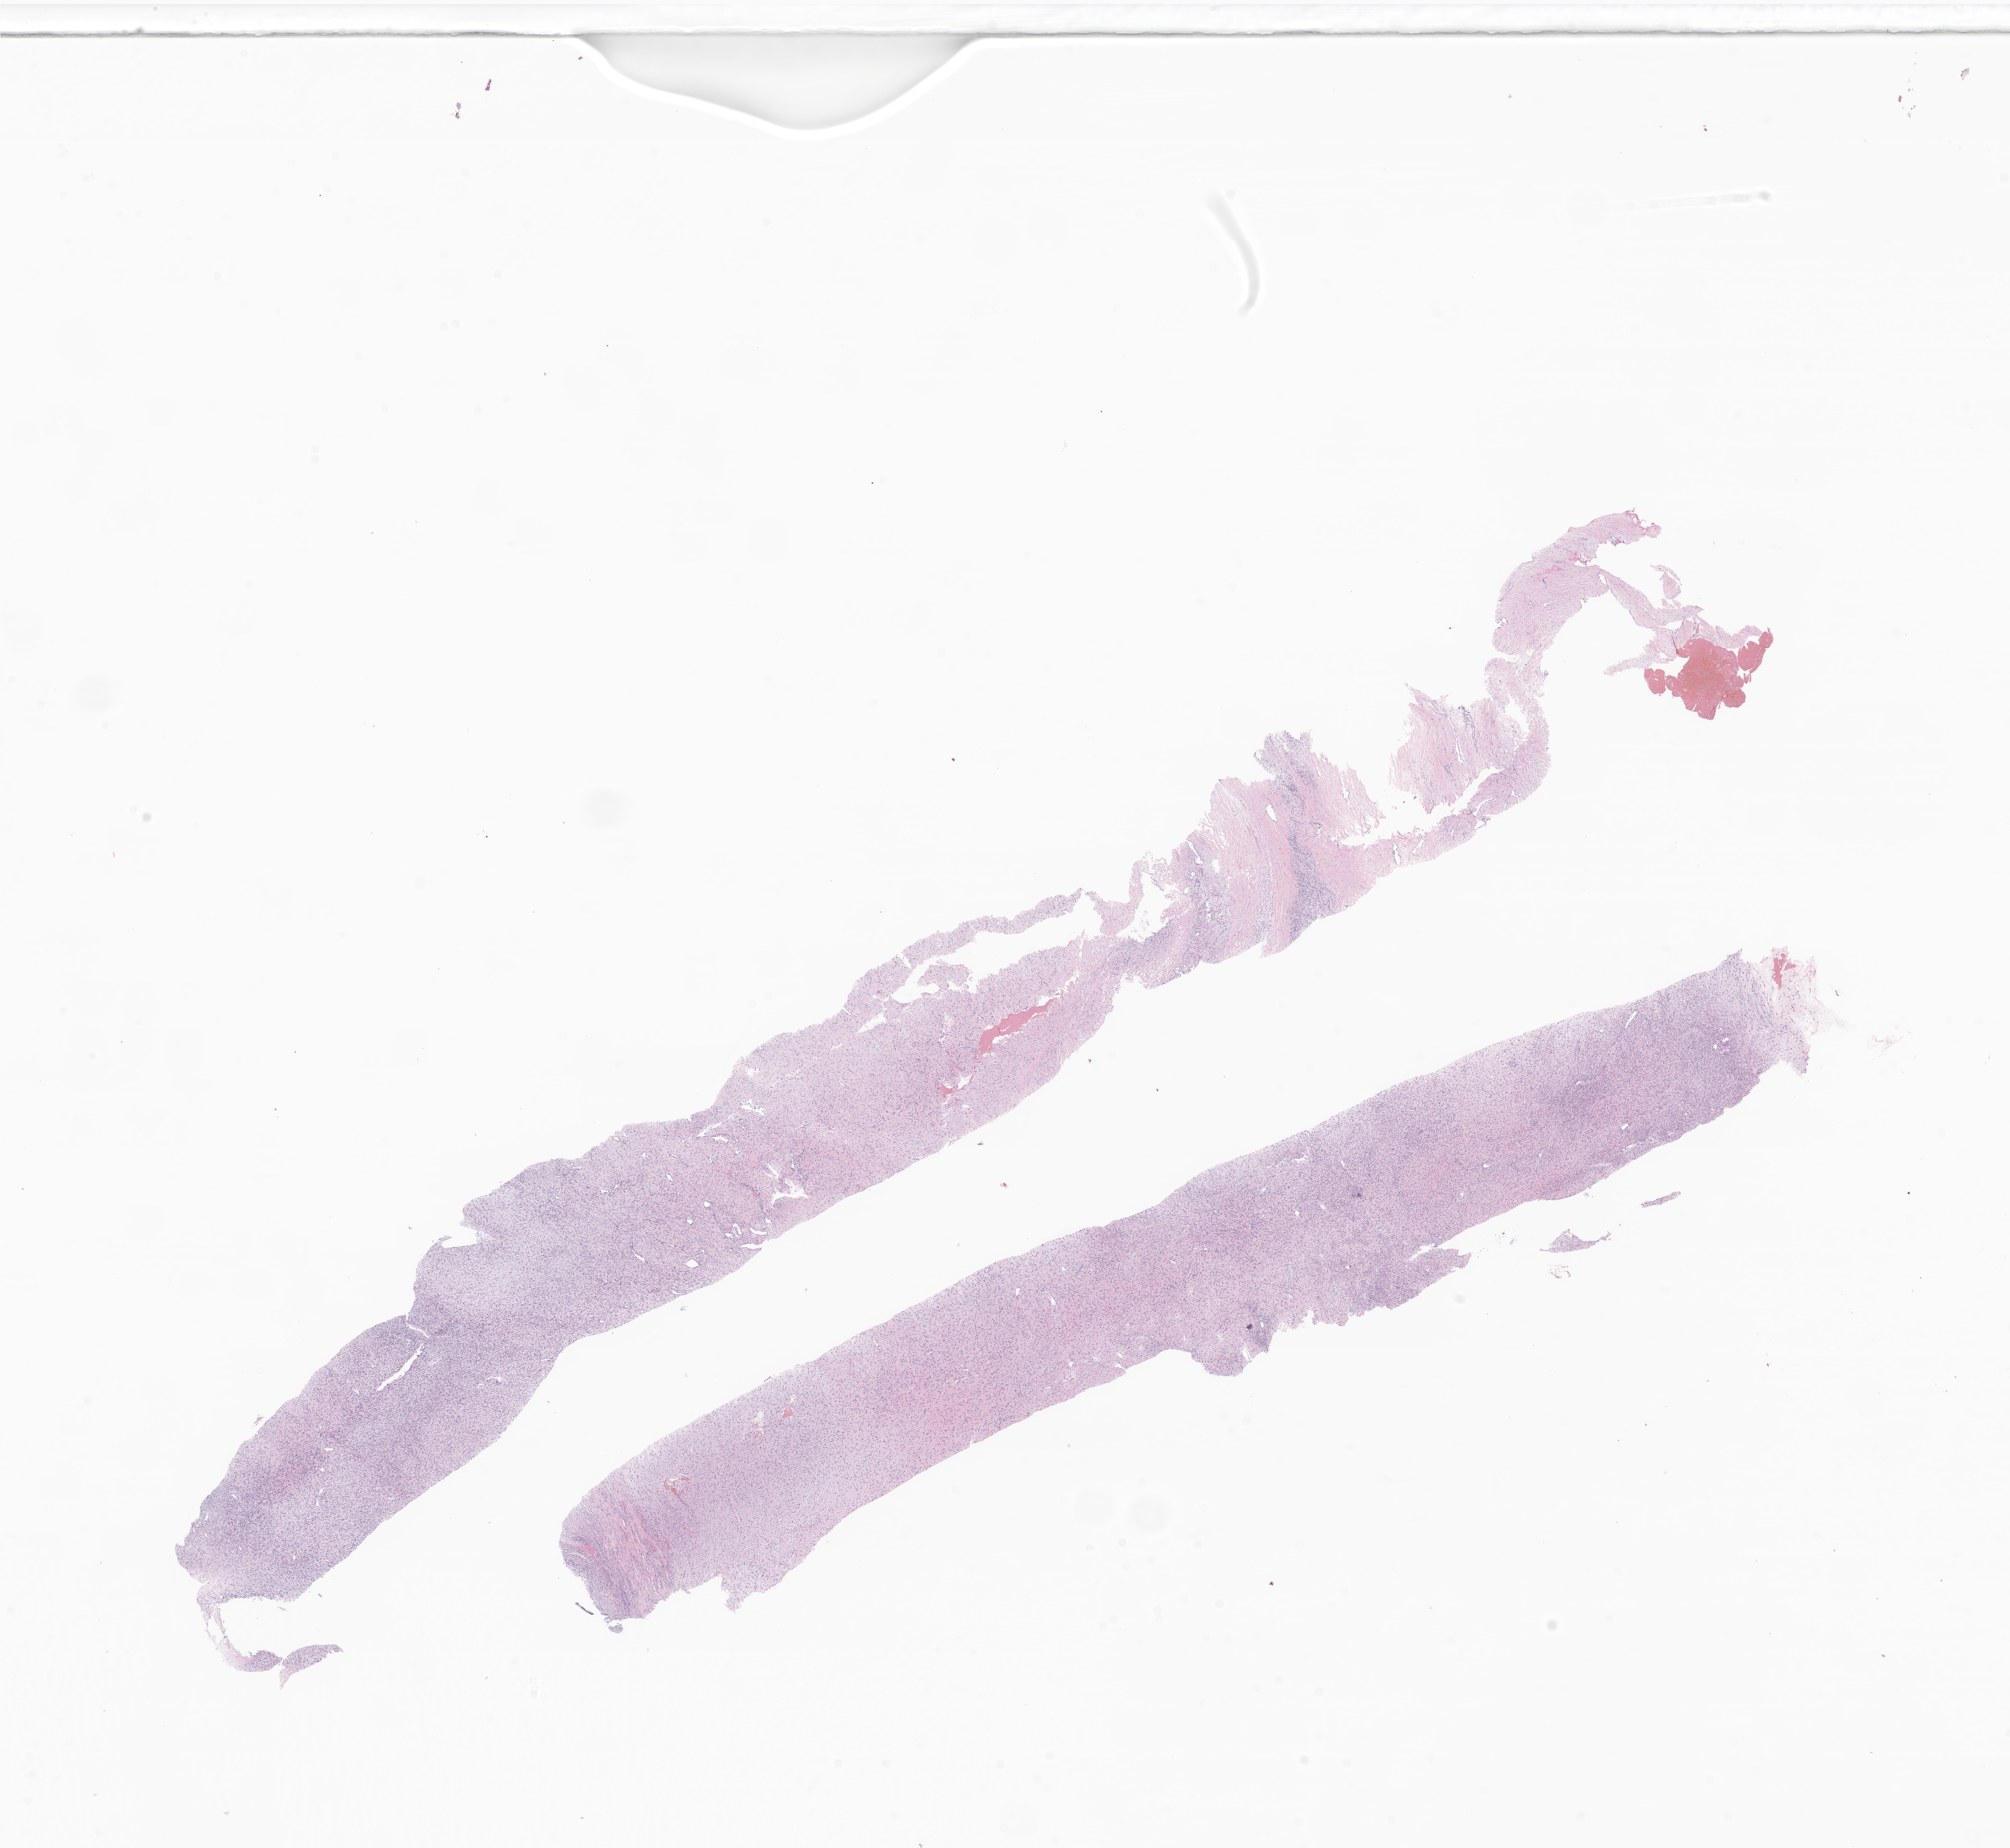
Whole-slide image, H&E stain of tumor tissue from the spinal cord, a low-resolution overview of the entire scanned area, about 21.3 x 19.6 mm; formalin-fixed, paraffin-embedded (FFPE) tissue. Patient: male, age 194 months (16 years 2 months).
• diagnosis (ICD-O-3 morphology term): Malignant peripheral nerve sheath tumor w. rhabdomyoblastic diff